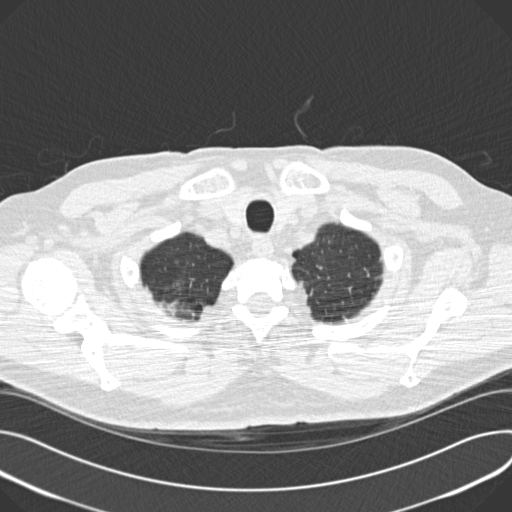
Low-dose screening chest CT, one axial slice. Lung window (W 1500 / L -600 HU). 2 mm slice thickness. 512 × 512 image matrix, field of view 376 × 376 mm.
Outlined on this slice (outlined manually by an expert reader):
- lesion 1 (tumor, upper lobe of right lung): bounding box (x1, y1, x2, y2) in pixels: (202, 306, 214, 314)